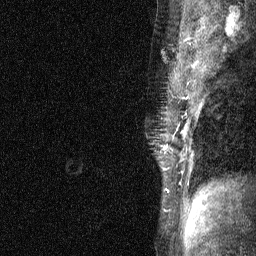
Breast MRI (dynamic contrast-enhanced), one sagittal slice; slice 48 of 64 in the series (ordered by position); dynamic contrast-enhanced study with each time point stored as its own series, time point 3 of 4 at this slice position (ordered by acquisition time); 1.5 T; TE 4.8 ms, TR 27 ms; 256 × 256 image matrix, field of view 180 × 180 mm. Female patient, age 44 years. From the clinical record (not read from this slice): setting: breast cancer imaged before/during neoadjuvant chemotherapy; receptor status: HR-positive, HER2-negative.
Structures marked on this image (semi-automatically segmented with operator editing):
- analysis volume of interest (the breast-tissue region the enhancement analysis was run in; not a lesion): bounding box (x1, y1, x2, y2) in pixels: (151, 117, 185, 188)
- tumour enhancement mask (voxels above the 90 % enhancement threshold inside the analysis volume of interest): (164, 131, 185, 149)